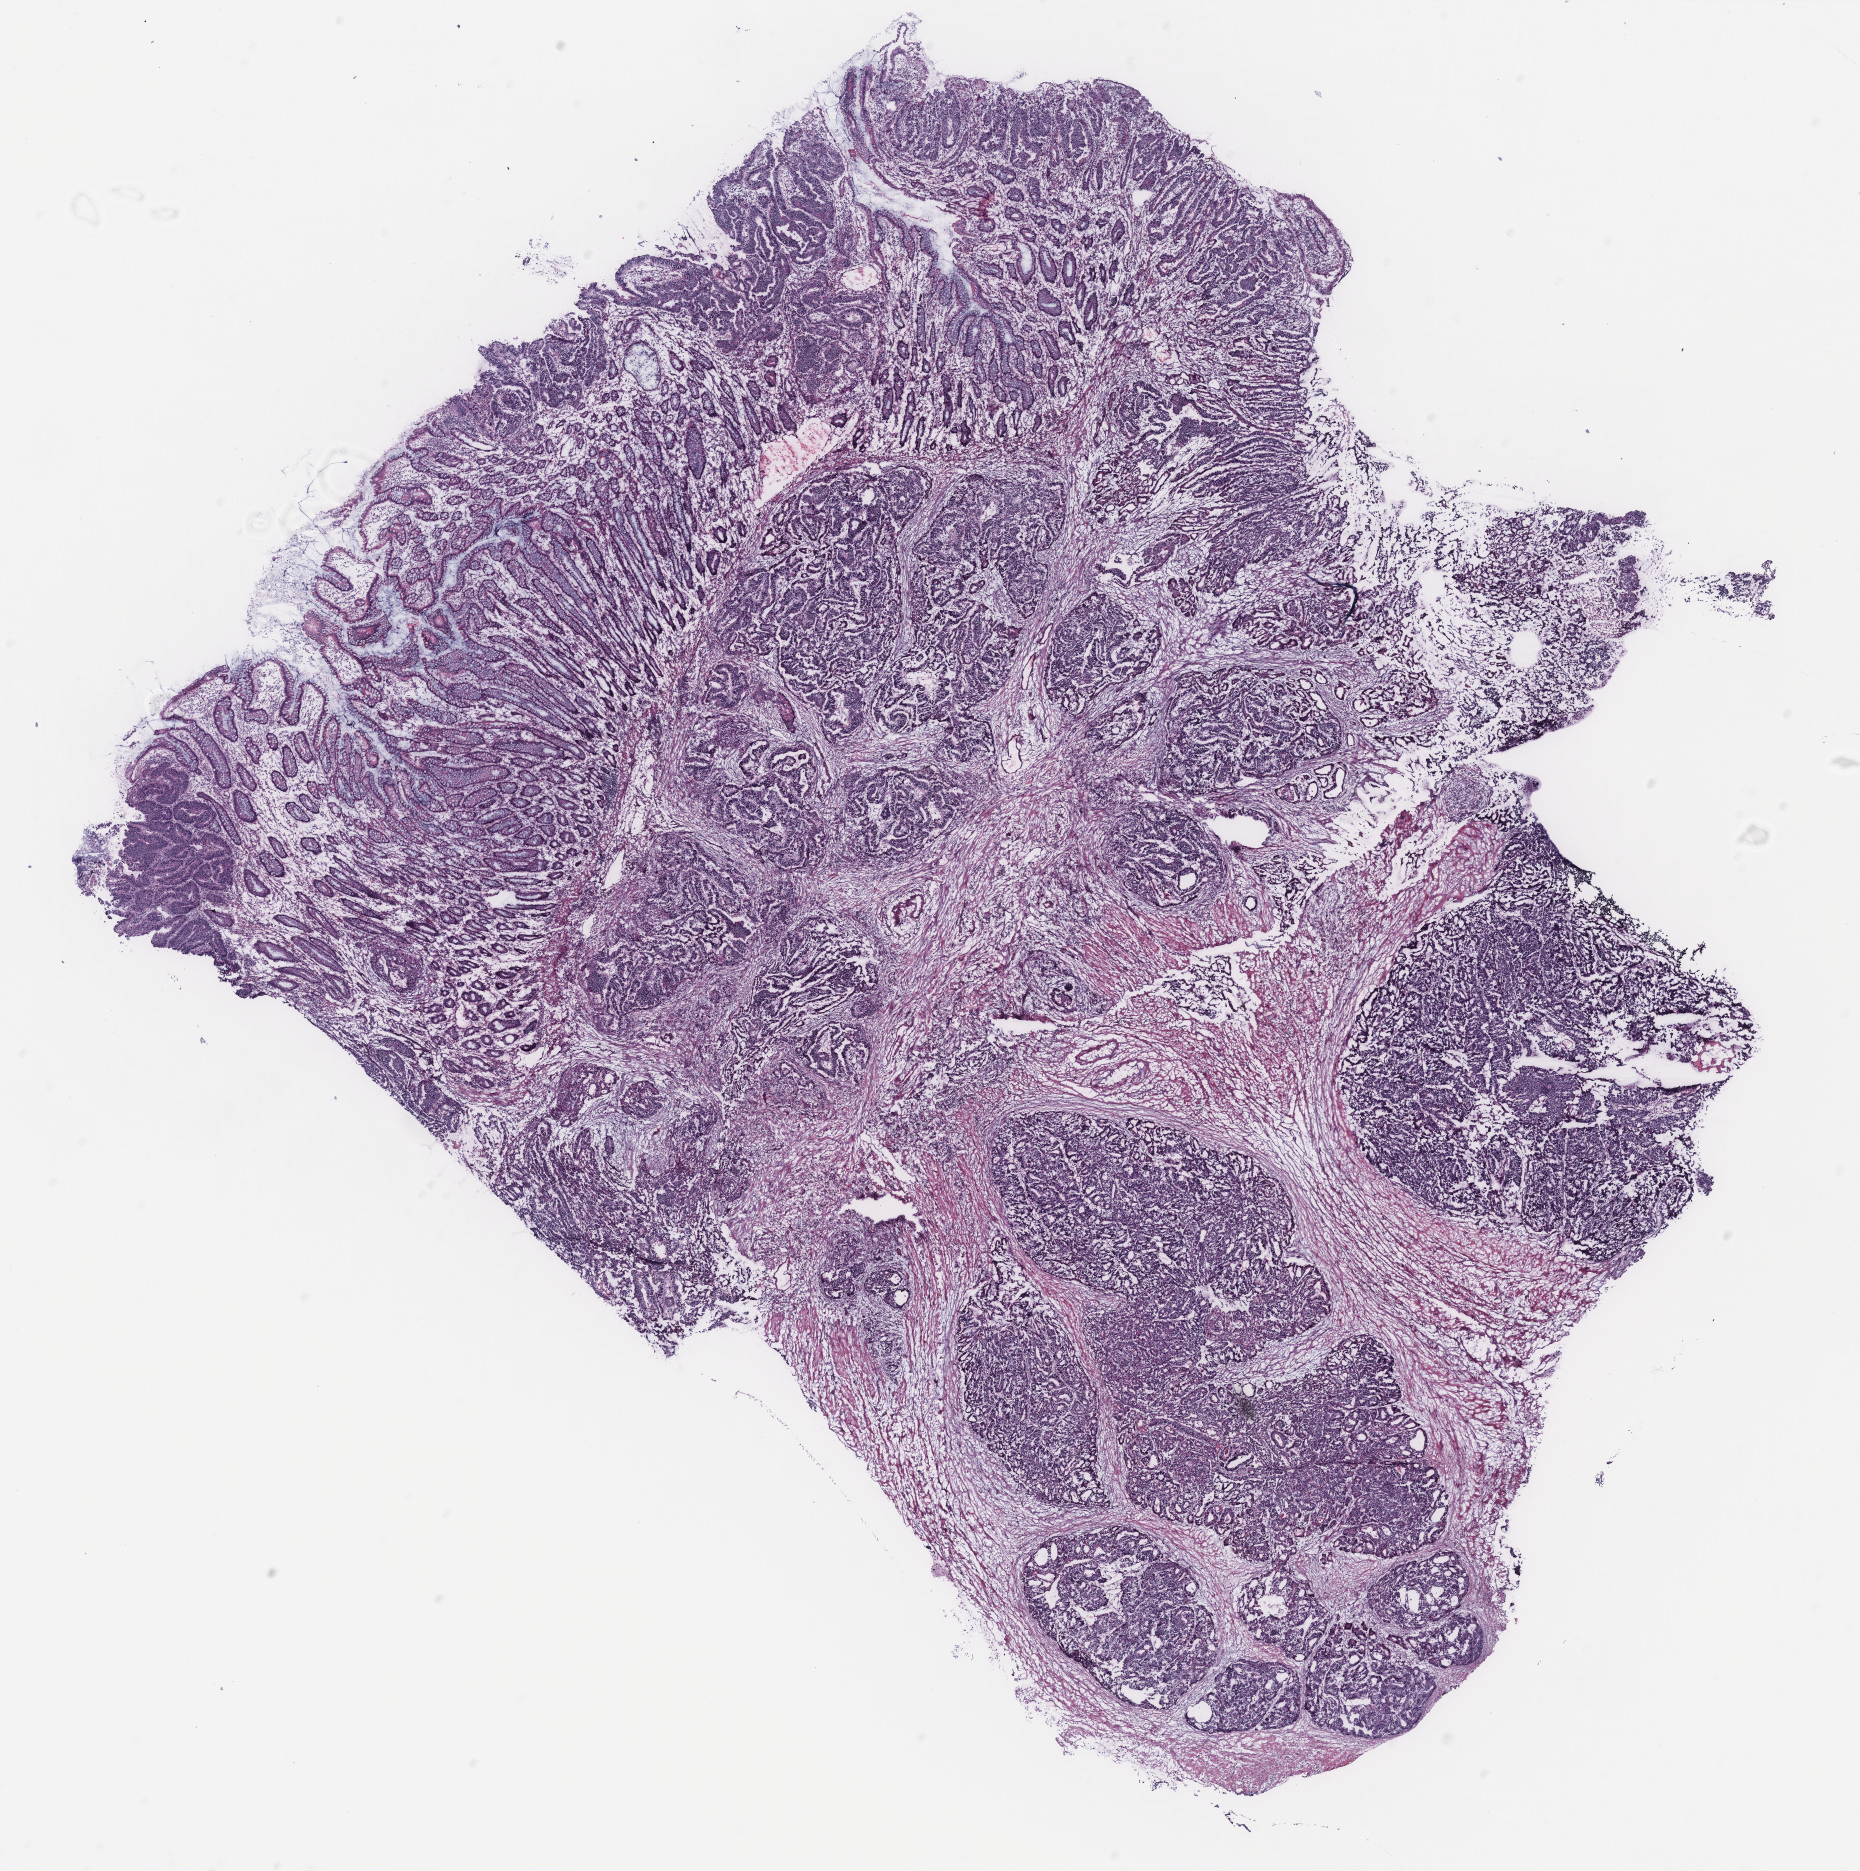
Digitized H&E tissue section (whole slide) — shown as a low-resolution overview of the whole scanned area (about 14.9 x 15.0 mm), colon, normal (non-tumour) tissue. Patient: male, age 75 years.
• this section: normal (non-tumour) tissue from the same patient
• patient diagnosis: Adenocarcinoma, NOS